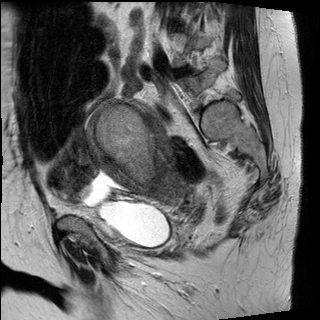
Pelvic MRI for cervical cancer, one sagittal slice; T2-weighted; 1.5 T; TE 89 ms, TR 2930 ms; 320 × 320 image matrix, field of view 260 × 260 mm. Patient: female, 62 years.
Outlined on this slice (outlined manually by an expert reader):
- uterus and cervix: bounding box (x1, y1, x2, y2) in pixels: (88, 97, 193, 204)